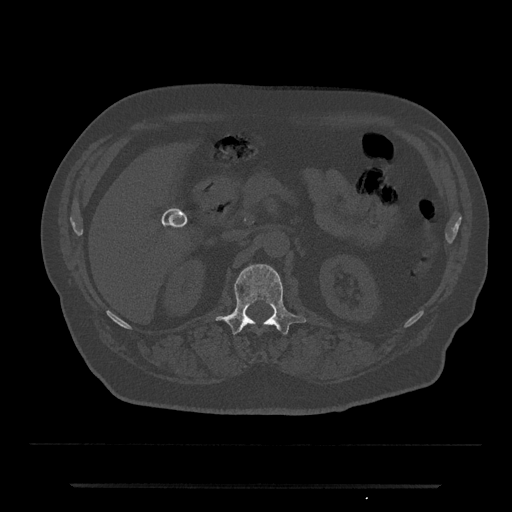
CT including the spine, one axial slice. Slice 544 of 797 in the series (ordered by position). Reconstruction kernel Br40s/3. Bone window (W 1800 / L 400 HU). 512 × 512 image matrix. Male patient, age 80 years. Case-level facts recorded for this patient, not image findings: primary cancer: prostate; vertebrae with lytic lesions (as recorded): L1, T11.
Annotated regions visible in this slice (semi-automatic segmentation, software-assisted and operator-edited):
- L1 vertebra: bounding box [x1, y1, x2, y2] px = [215, 264, 306, 334]